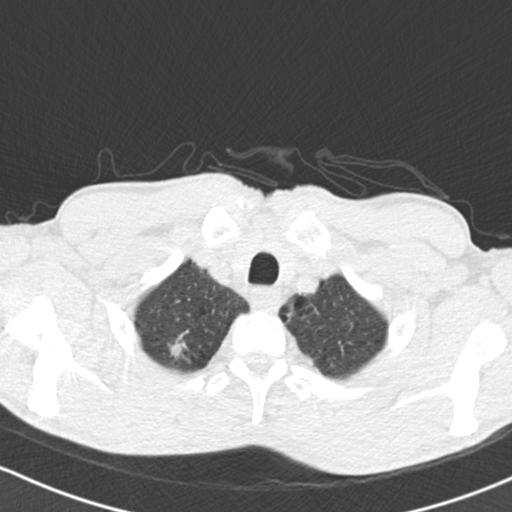
Low-dose screening chest CT, one axial slice. Slice 126 of 150 in the series (ordered by position). Reconstruction kernel B30f. 120 kVp. Lung window (W 1500 / L -600 HU). 2 mm slice thickness. 512 × 512 image matrix, field of view 312 × 312 mm.
Structures marked on this image (outlined manually by an expert reader):
- lesion 1 (tumor, upper lobe of right lung): box from (x=171, y=342) to (x=185, y=357) px